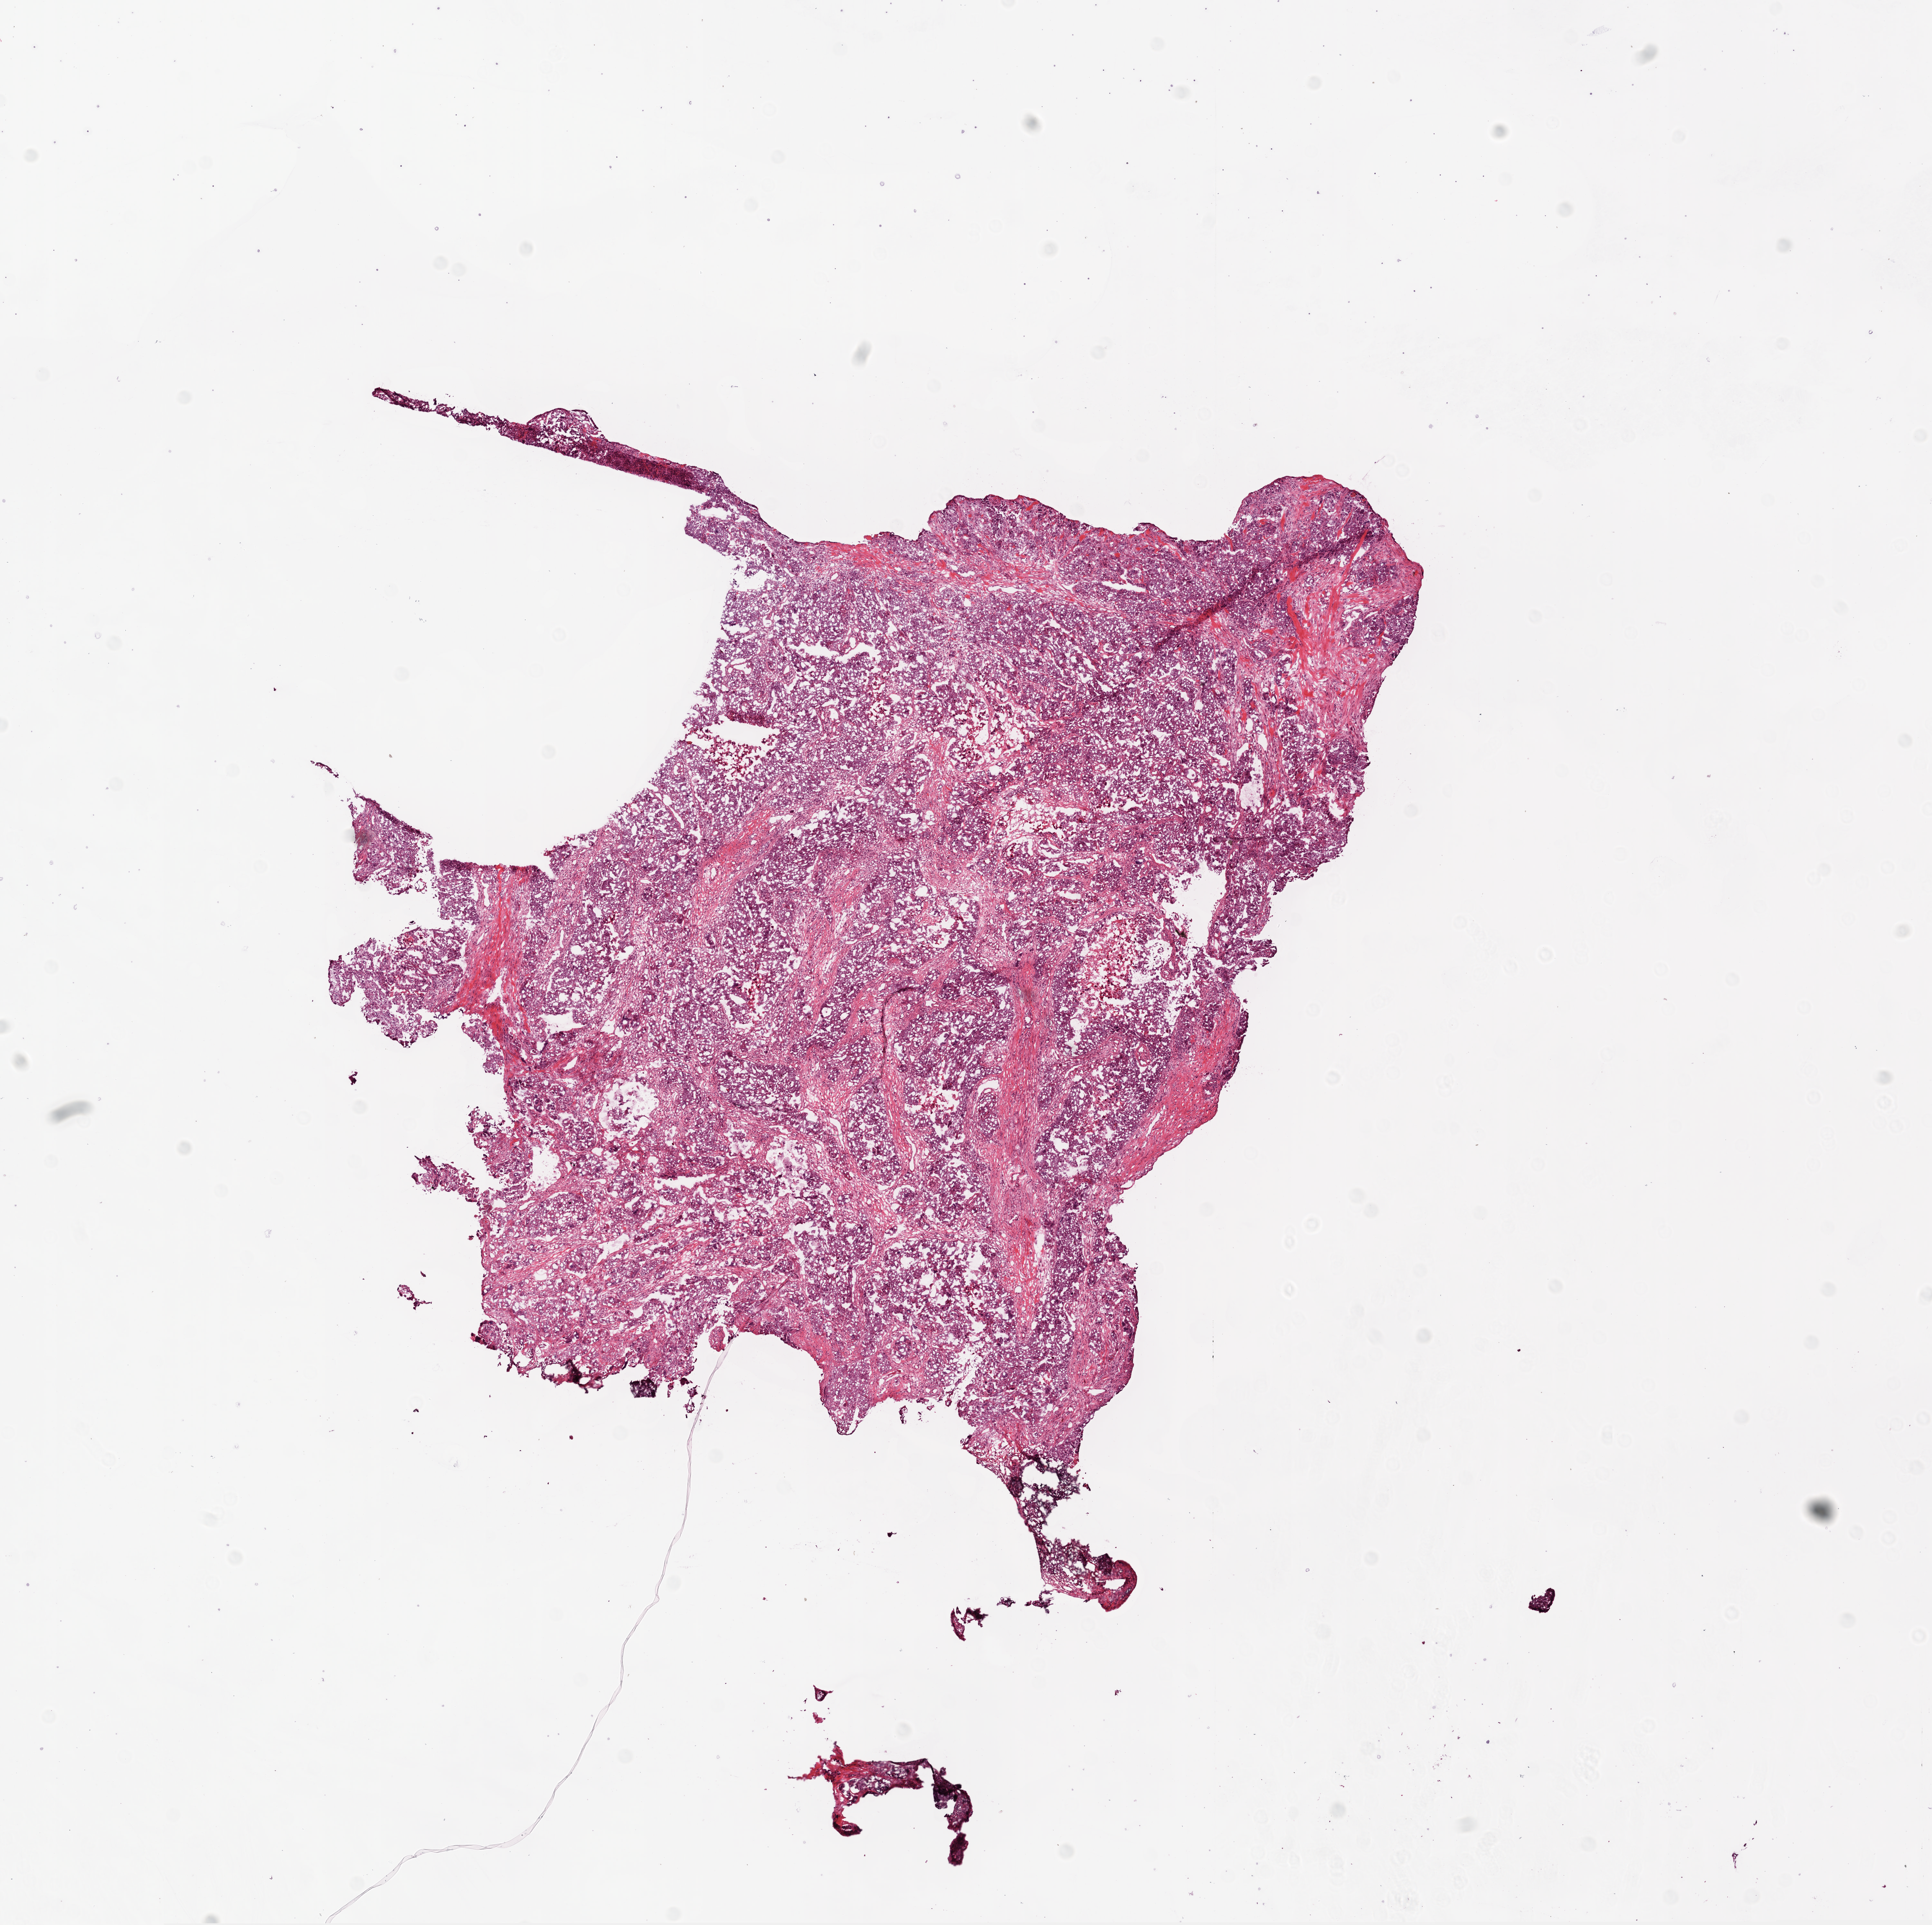
Whole-slide histology image, H&E-stained — a low-resolution overview of the entire scanned area, about 12.0 x 12.0 mm. Frozen section from the bottom of the tissue portion. Ovary, recurrent tumour sample. Female, age 58 years at initial diagnosis. Composition of this section per pathologist review: tumour cells 80%, tumour nuclei 90%, normal cells 0%, stromal cells 15%, necrosis 5%.
- this section: recurrent tumour
- patient diagnosis: Serous cystadenocarcinoma, NOS